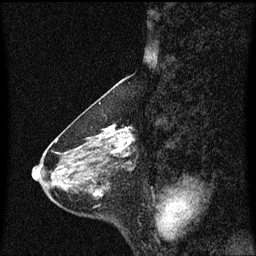
Breast MRI (dynamic contrast-enhanced), one sagittal slice. Position 25 of 60 along the scan axis. Dynamic contrast-enhanced series, image 2 of 3 at this slice position (ordered by acquisition). 1.5 T. TE 4.2 ms, TR 8.4 ms. 2 mm slice thickness. 256 × 256 image matrix. Patient: female, 58 years.
Structures marked on this image (semi-automatically segmented with operator editing):
- analysis volume of interest (the breast-tissue region the enhancement analysis was run in; not a lesion): bounding box <100,124,135,160> (left, top, right, bottom; pixels)
- tumour enhancement mask (voxels above the 70 % enhancement threshold inside the analysis volume of interest): <100,124,135,156>